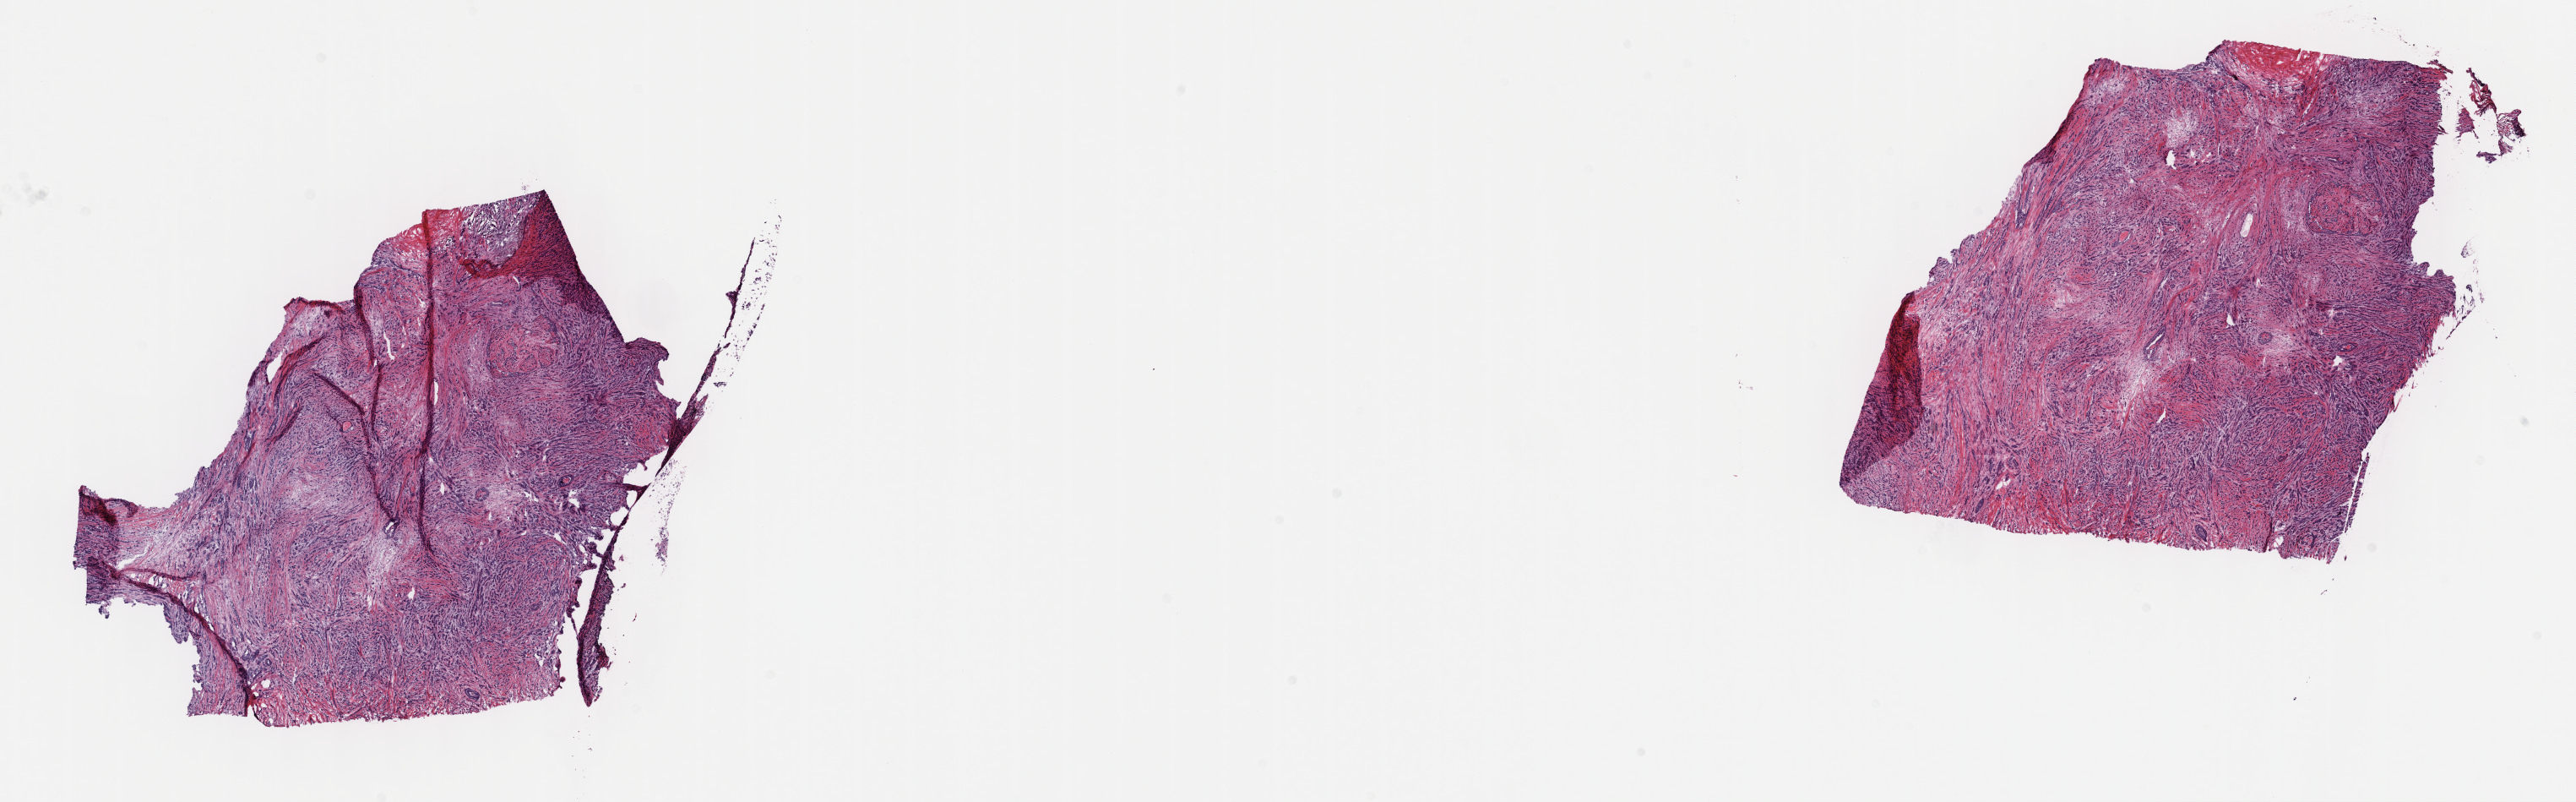
Digitized H&E tissue section (whole slide), shown as a low-resolution overview of the whole scanned area (about 24.7 x 7.7 mm); frozen section from the top of the tissue portion; breast, primary tumour sample. Female patient; age at initial diagnosis 50 years. Slide review estimates, as recorded: tumour cells 70%, tumour nuclei 70%, normal cells 10%, stromal cells 20%, necrosis 0%. Inflammatory infiltration, as recorded: lymphocyte infiltration 5%, monocyte infiltration 0%, neutrophil infiltration 0%.
Laterality: left. Lymph nodes positive (case pathology): 4 of 14 examined. TNM: T2 N2a M0. AJCC pathologic stage: IIIA. Diagnosis: Lobular carcinoma, NOS.